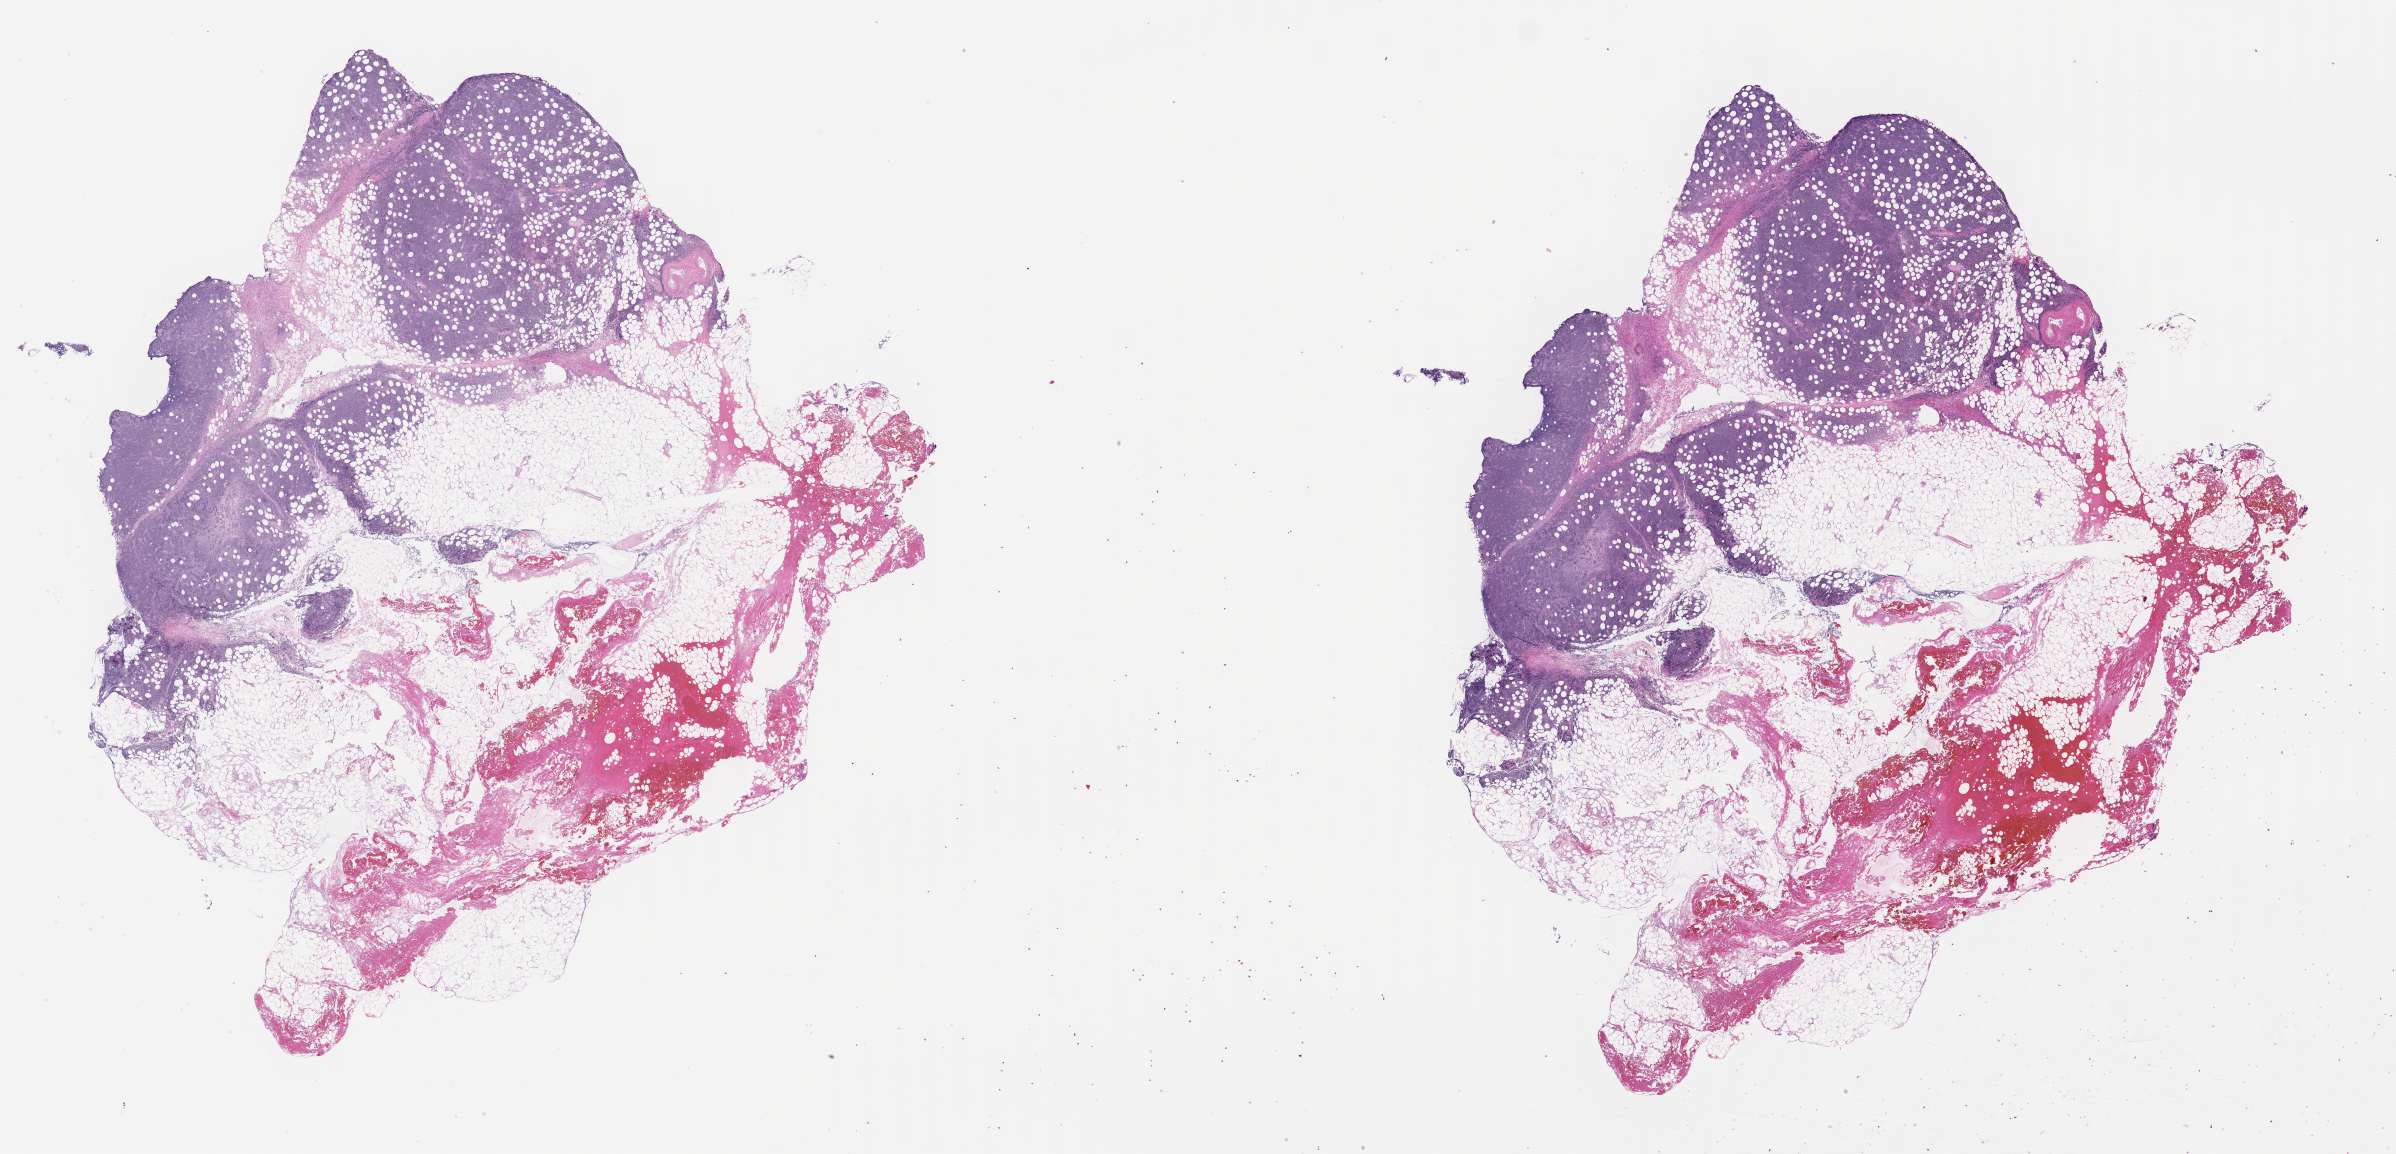
Whole-slide image, haematoxylin and eosin stain, shown as a low-resolution overview of the whole scanned area (about 38.7 x 18.7 mm), formalin-fixed, paraffin-embedded (FFPE) tissue, primary tumor, site: upper limb lymph node. Male patient, 76 years old. Slide review estimates, as recorded: tumor cells 35%, tumor nuclei 80%, stromal cells 20%, necrosis 5%, normal cells 40%. Inflammatory infiltration, as recorded: lymphocyte infiltration 15%, monocyte infiltration 25%, neutrophil infiltration 15%.
* section: top of the tissue portion
* Ann Arbor stage (patient): Stage I
* diagnosis: Burkitt lymphoma, NOS